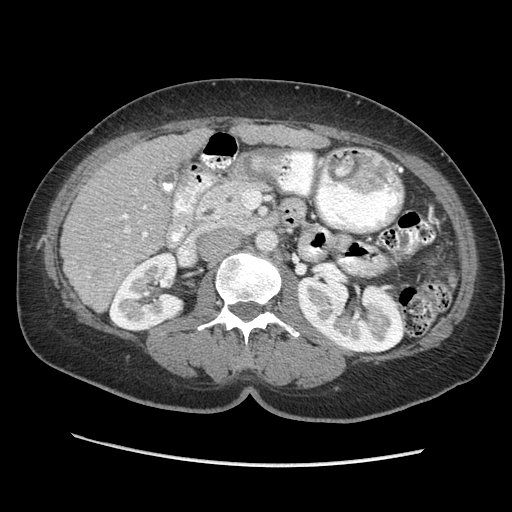
Contrast-enhanced abdominal CT (liver protocol), one axial slice; slice 111 of 170 in the series (ordered by position); 140 kVp; soft-tissue window (W 400 / L 40 HU); 2.5 mm slice thickness; 512 × 512 image matrix, field of view 360 × 360 mm. From the clinical record (not read from this slice): diagnosis: hepatocellular carcinoma (patient treated with transarterial chemoembolisation; whether this scan precedes or follows treatment is not stated here); TNM stage (as recorded): Stage-II.
Annotated regions visible in this slice (semi-automatic segmentation, software-assisted and operator-edited):
- liver parenchyma outside the tumour (the mass and vessels are separate outlines, so this box may not span the whole liver): box from (x=60, y=122) to (x=324, y=312) px
- liver vessels: (x=114, y=205)–(x=148, y=260)